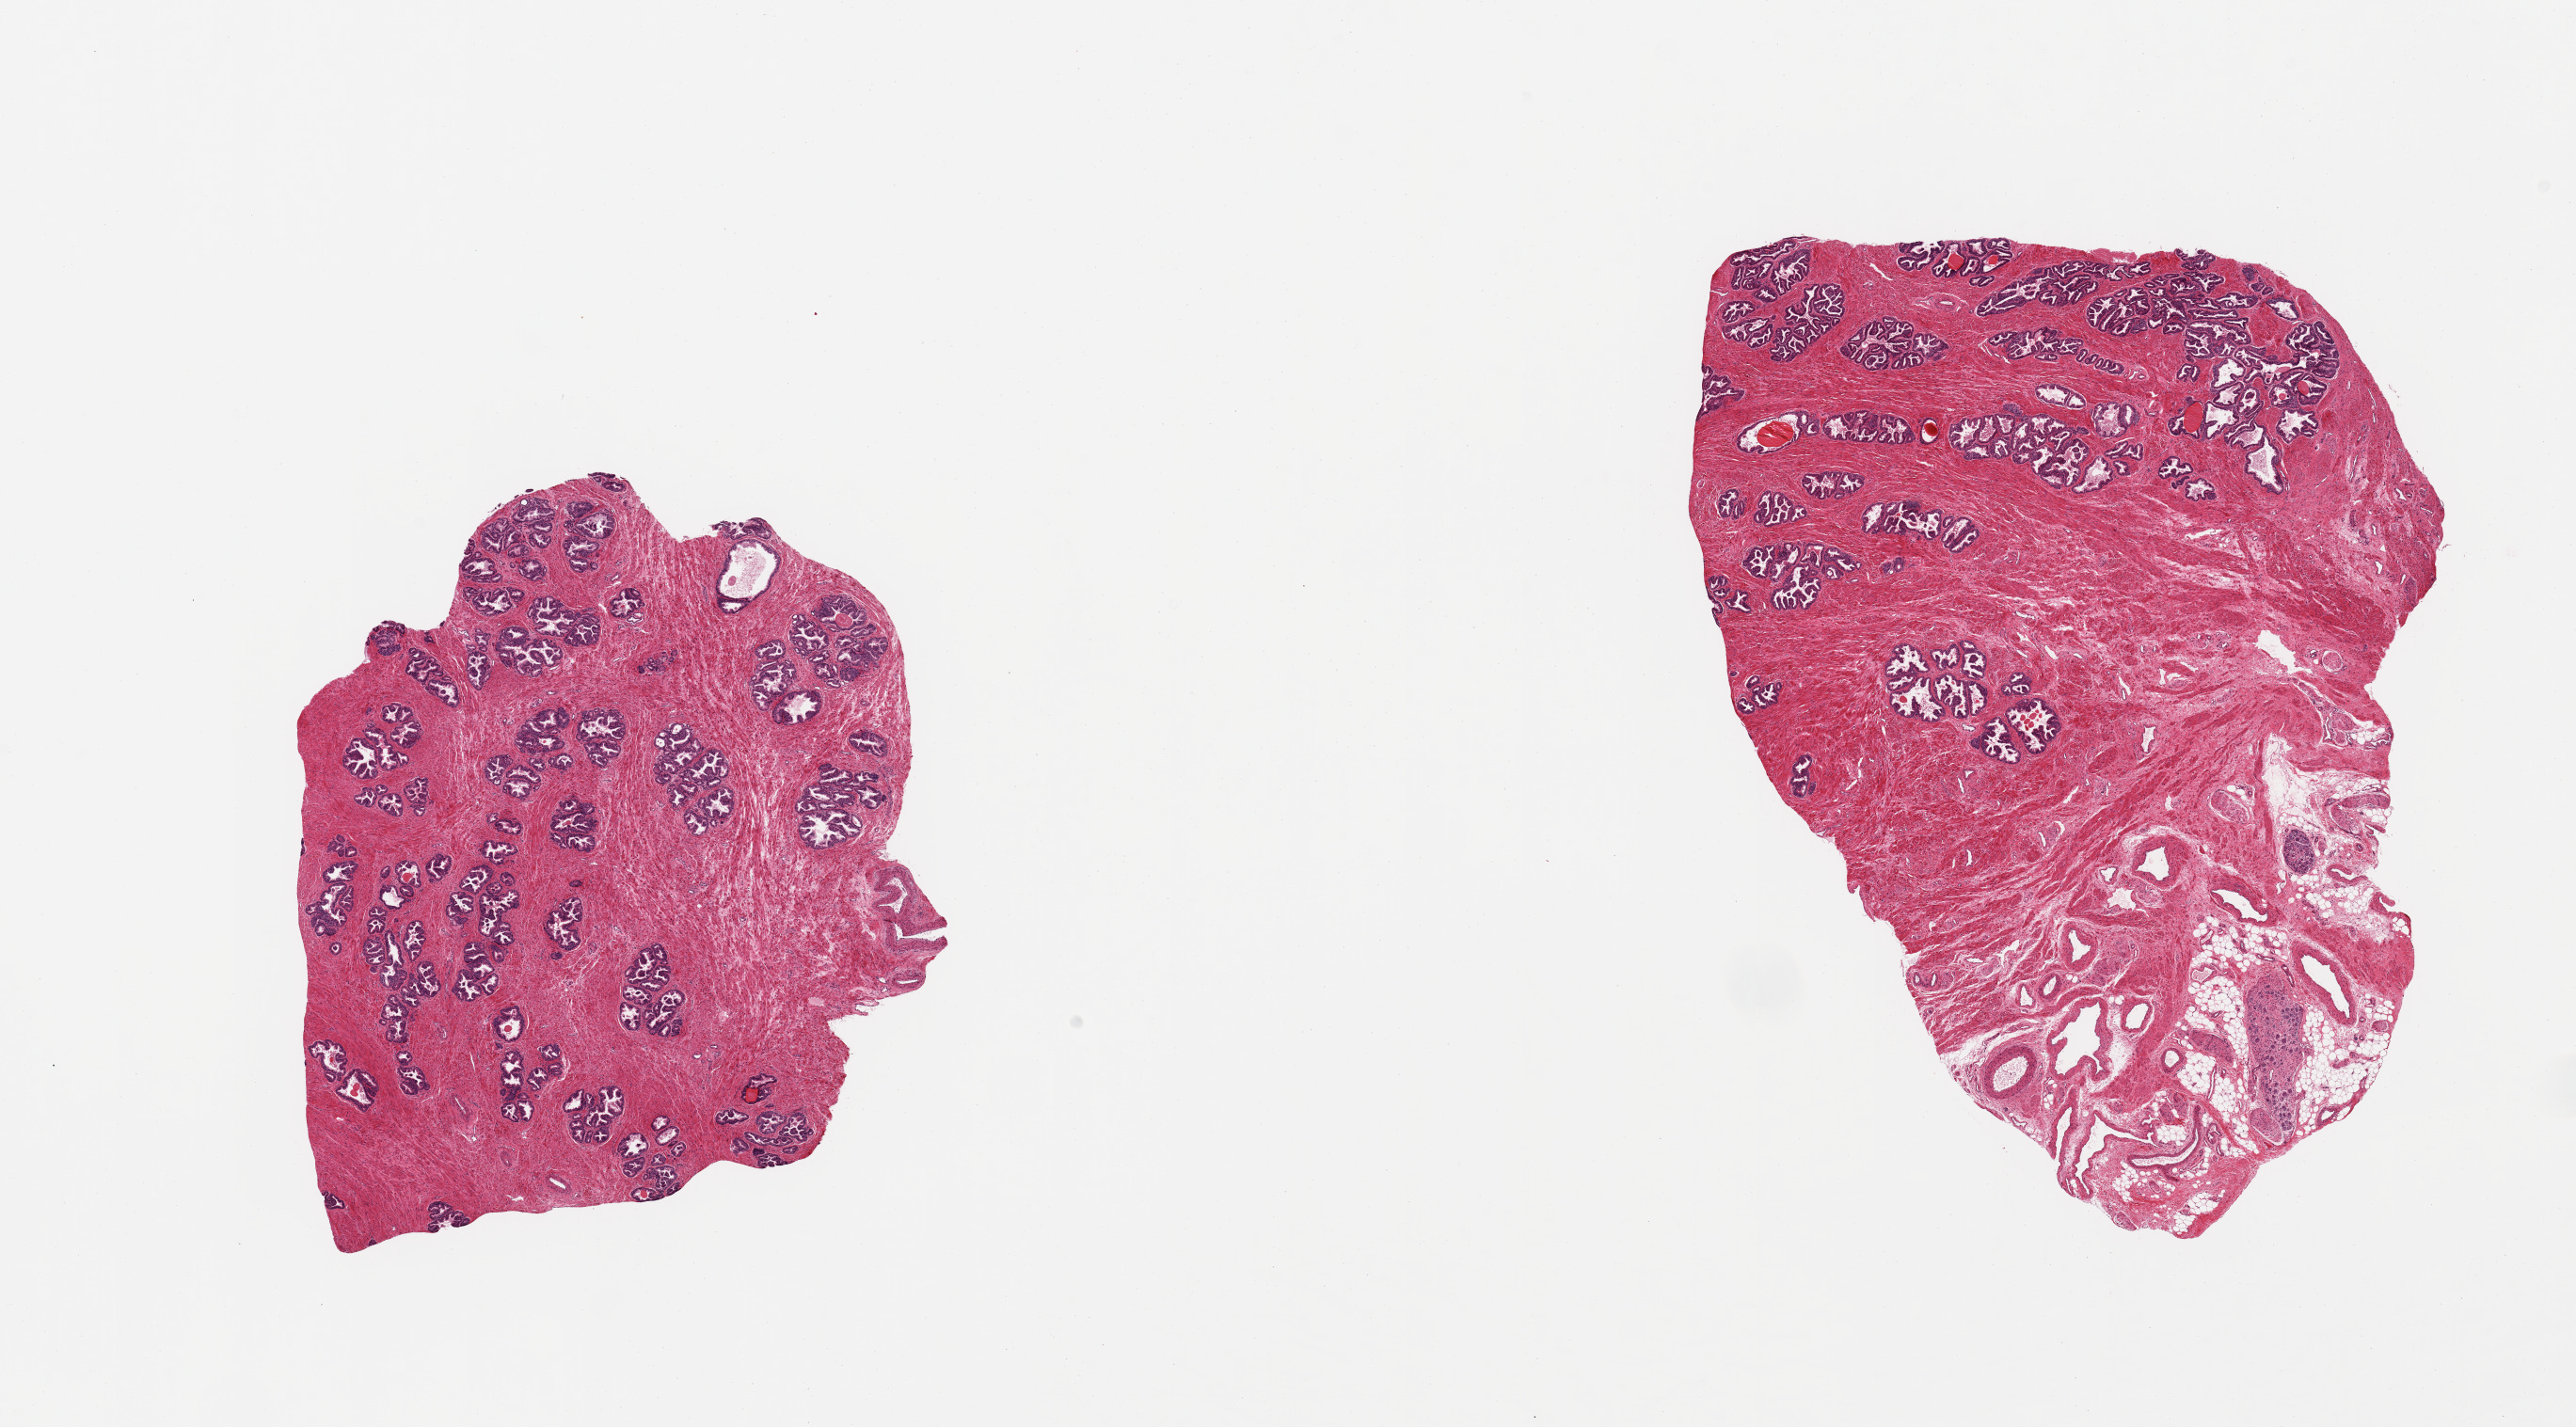
Hematoxylin and eosin (H&E) whole-slide image — a low-resolution overview of the entire scanned area, about 21.7 x 12.0 mm (acquisition: 20x scan), PAXgene-fixed, paraffin-embedded tissue, section of prostate (target tissue), tissue donor sample. Donor: male.
Reviewer comment on this tissue sample: 2 pieces, glandular hyperplasia; ~25% adherent fat, nerve elements.